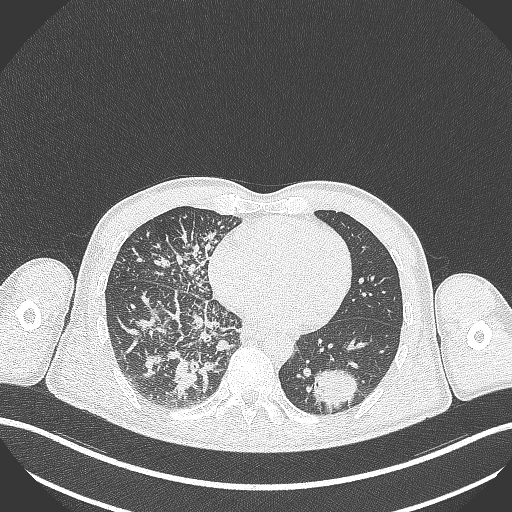
Chest CT, one axial slice. Position 113 of 348 along the scan axis. Reconstruction kernel B70f. 120 kVp. Lung window (W 1500 / L -600 HU). 1 mm slice thickness. 512 × 512 image matrix, field of view 400 × 400 mm. Patient: male, 49 years. Case-level facts recorded for this patient, not image findings: clinical TNM (as recorded): T2b N1 M0.
Outlined on this slice (bounding box drawn by a radiologist):
- lung tumour (recorded histology: adenocarcinoma): box from (x=309, y=366) to (x=363, y=416) px